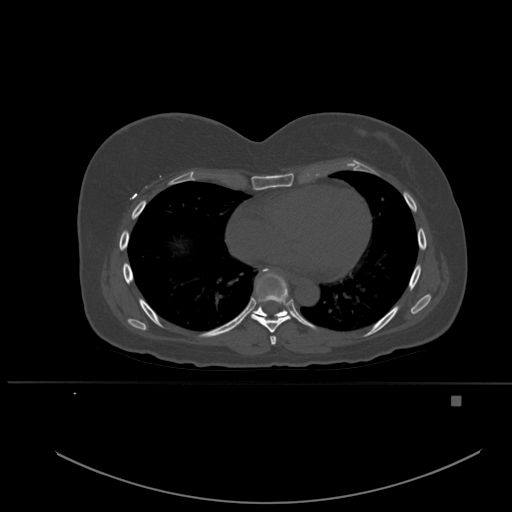
CT including the spine, one axial slice. Bone window (W 1800 / L 400 HU). 1.5 mm slice thickness. 512 × 512 image matrix, field of view 443 × 443 mm. Female patient, age 49 years. From the clinical record (not read from this slice): primary cancer: breast.
Structures marked on this image (semi-automatic segmentation, software-assisted and operator-edited):
- T6 vertebra: box from (x=270, y=335) to (x=277, y=345) px
- T7 vertebra: (x=251, y=272)–(x=292, y=333)
- T8 vertebra: (x=253, y=268)–(x=292, y=318)